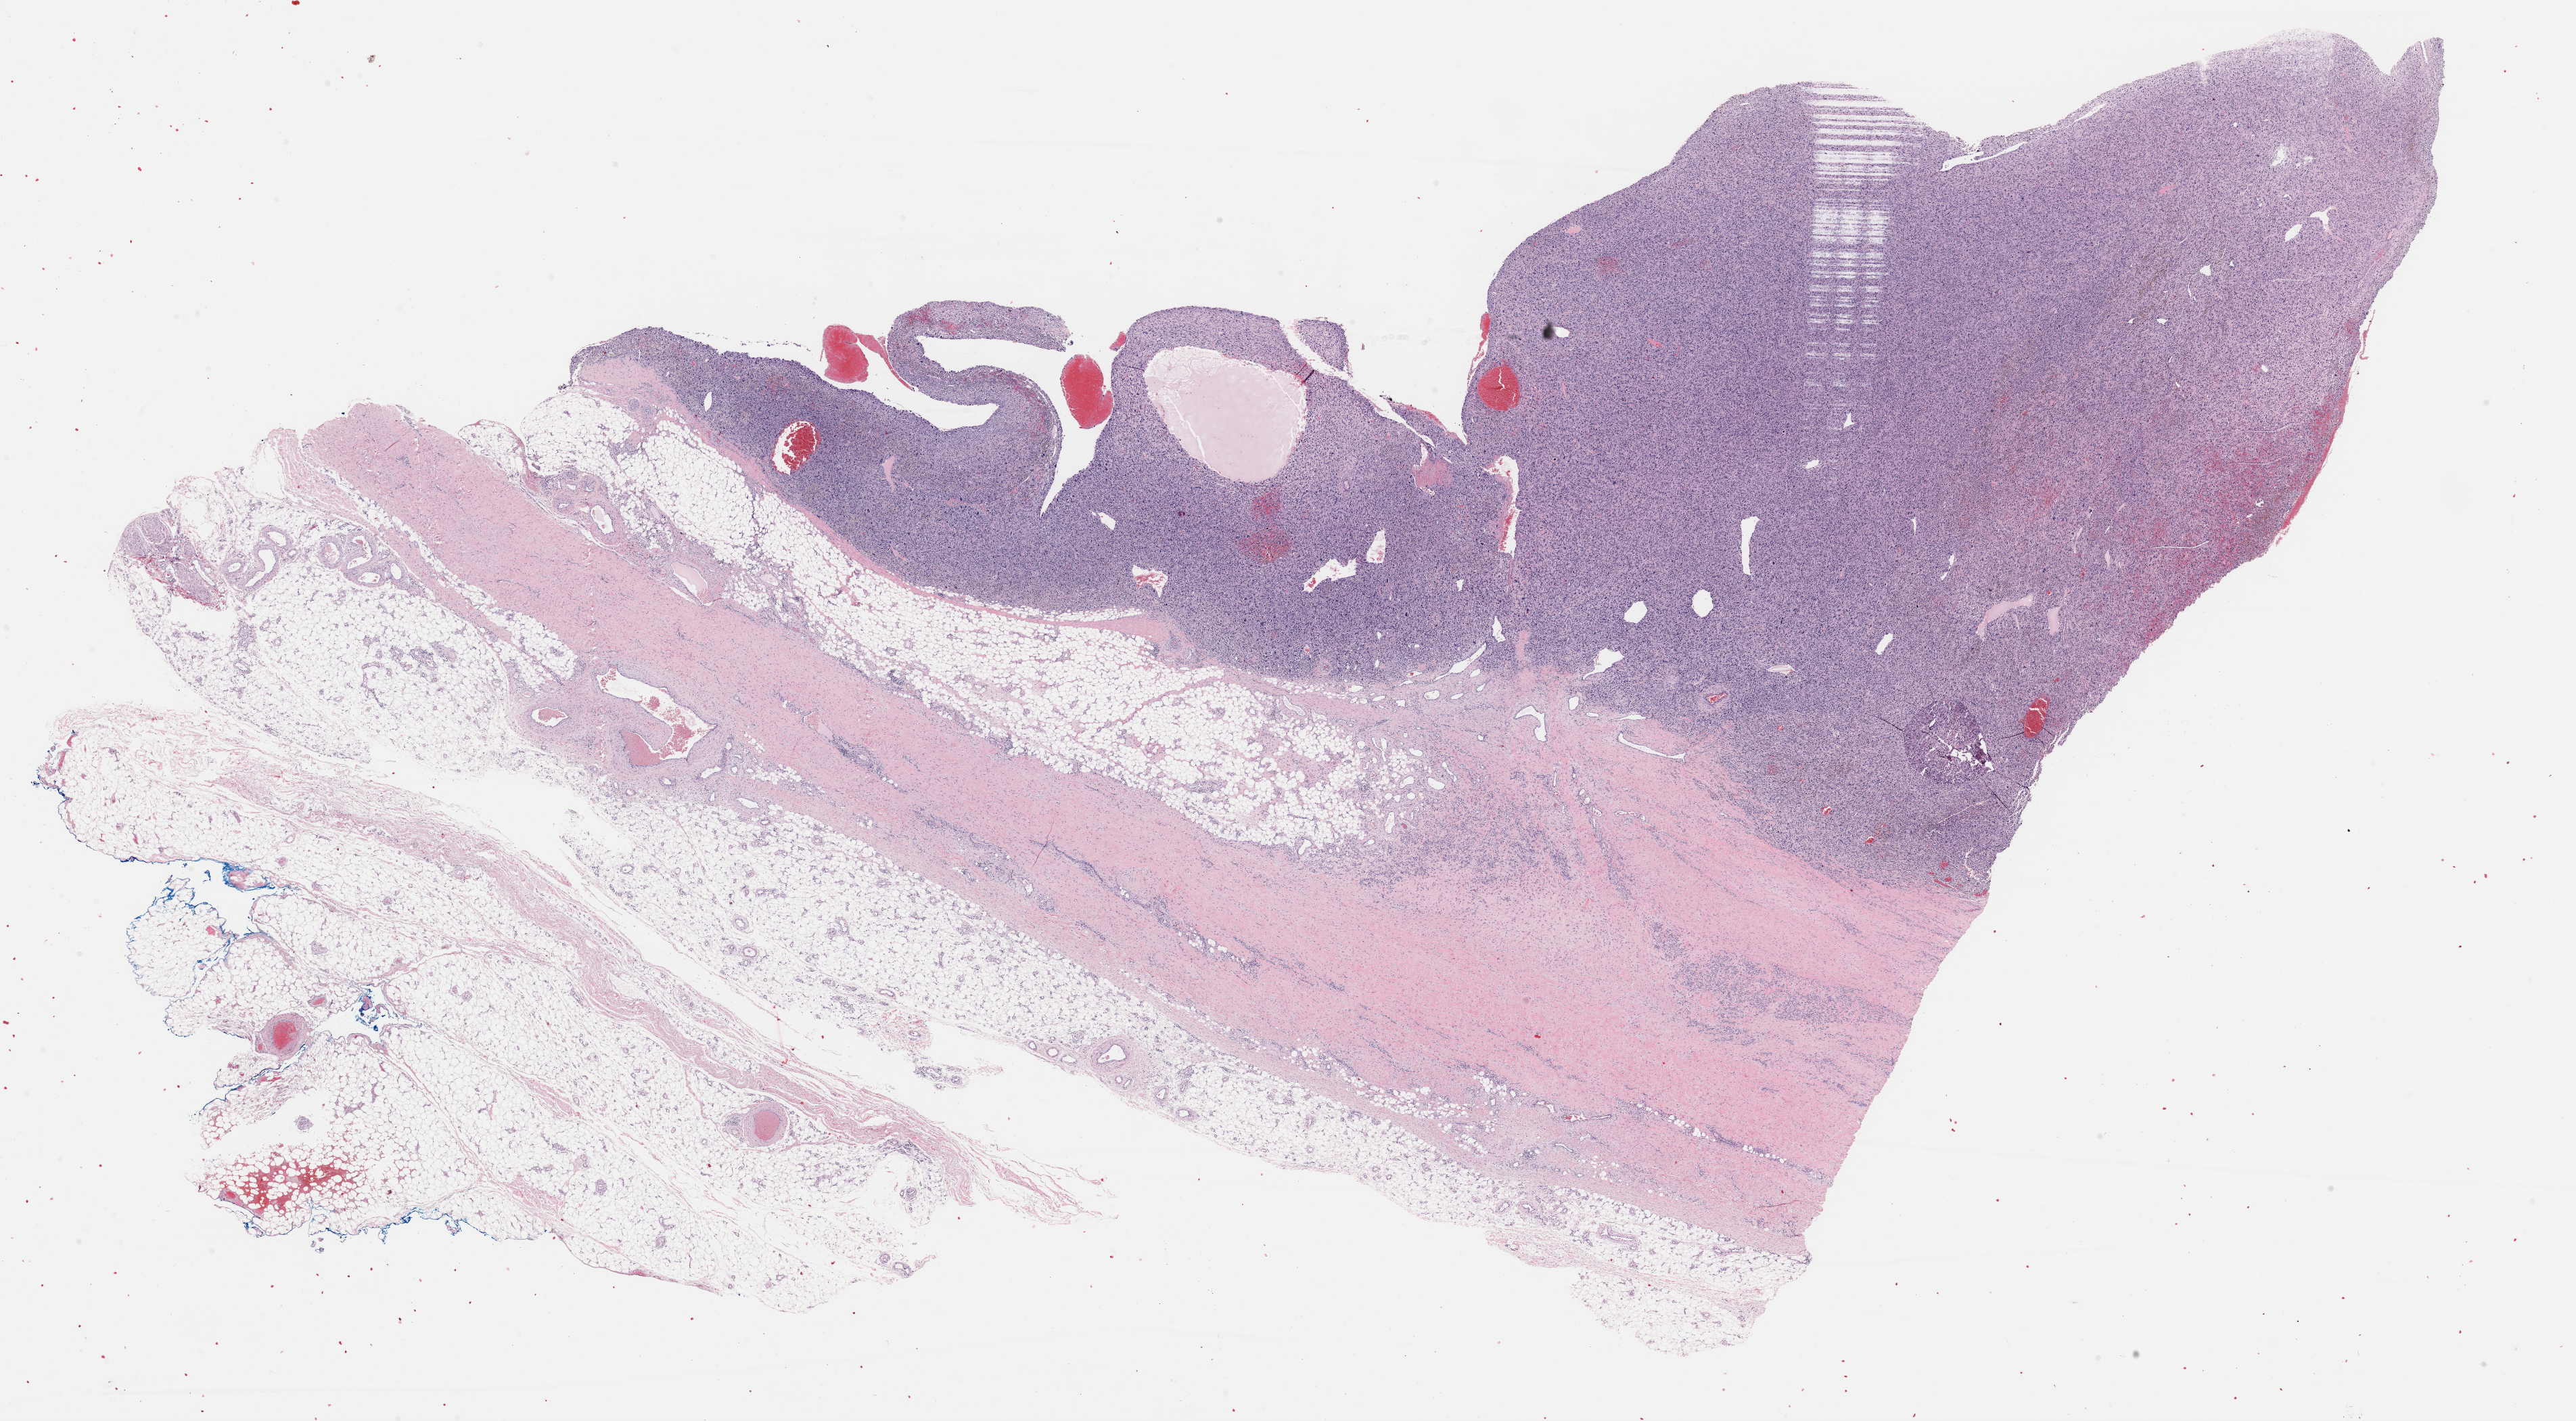
Hematoxylin and eosin (H&E) stained whole-slide image — whole scanned area (about 30.1 x 16.6 mm, acquisition: 40x scan) shown as a low-resolution overview; FFPE section; sample: primary tumour, connective, subcutaneous and other soft tissues. Female patient; age at initial diagnosis 75 years.
Histologic diagnosis: Malignant fibrous histiocytoma (connective, subcutaneous and other soft tissues of lower limb and hip).